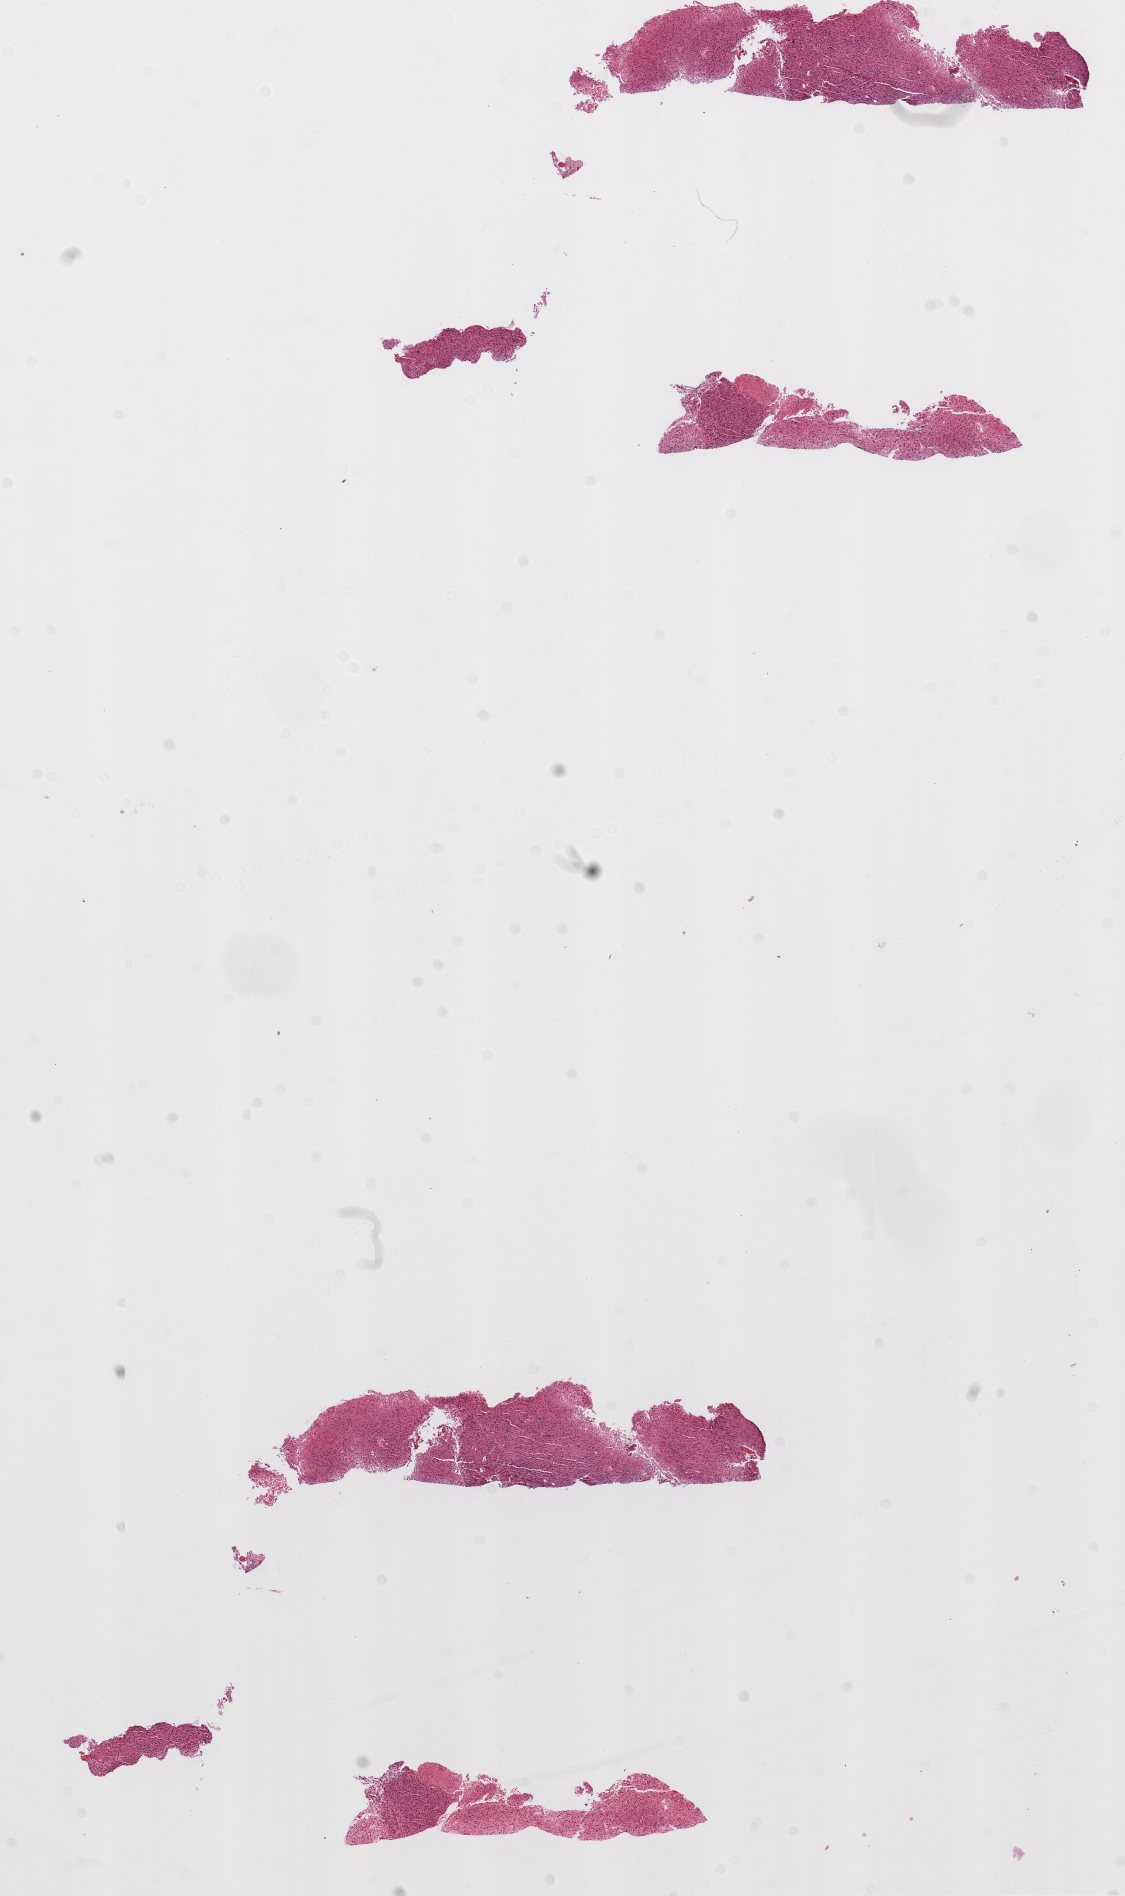
Digitized H&E tissue section (whole slide), a low-resolution overview of the entire scanned area, about 9.0 x 15.2 mm (from a 20x scan), formalin-fixed paraffin-embedded (FFPE) diagnostic section, primary tumour sample from the brain. Male patient; age at initial diagnosis 67 years.
- diagnosis: Glioblastoma